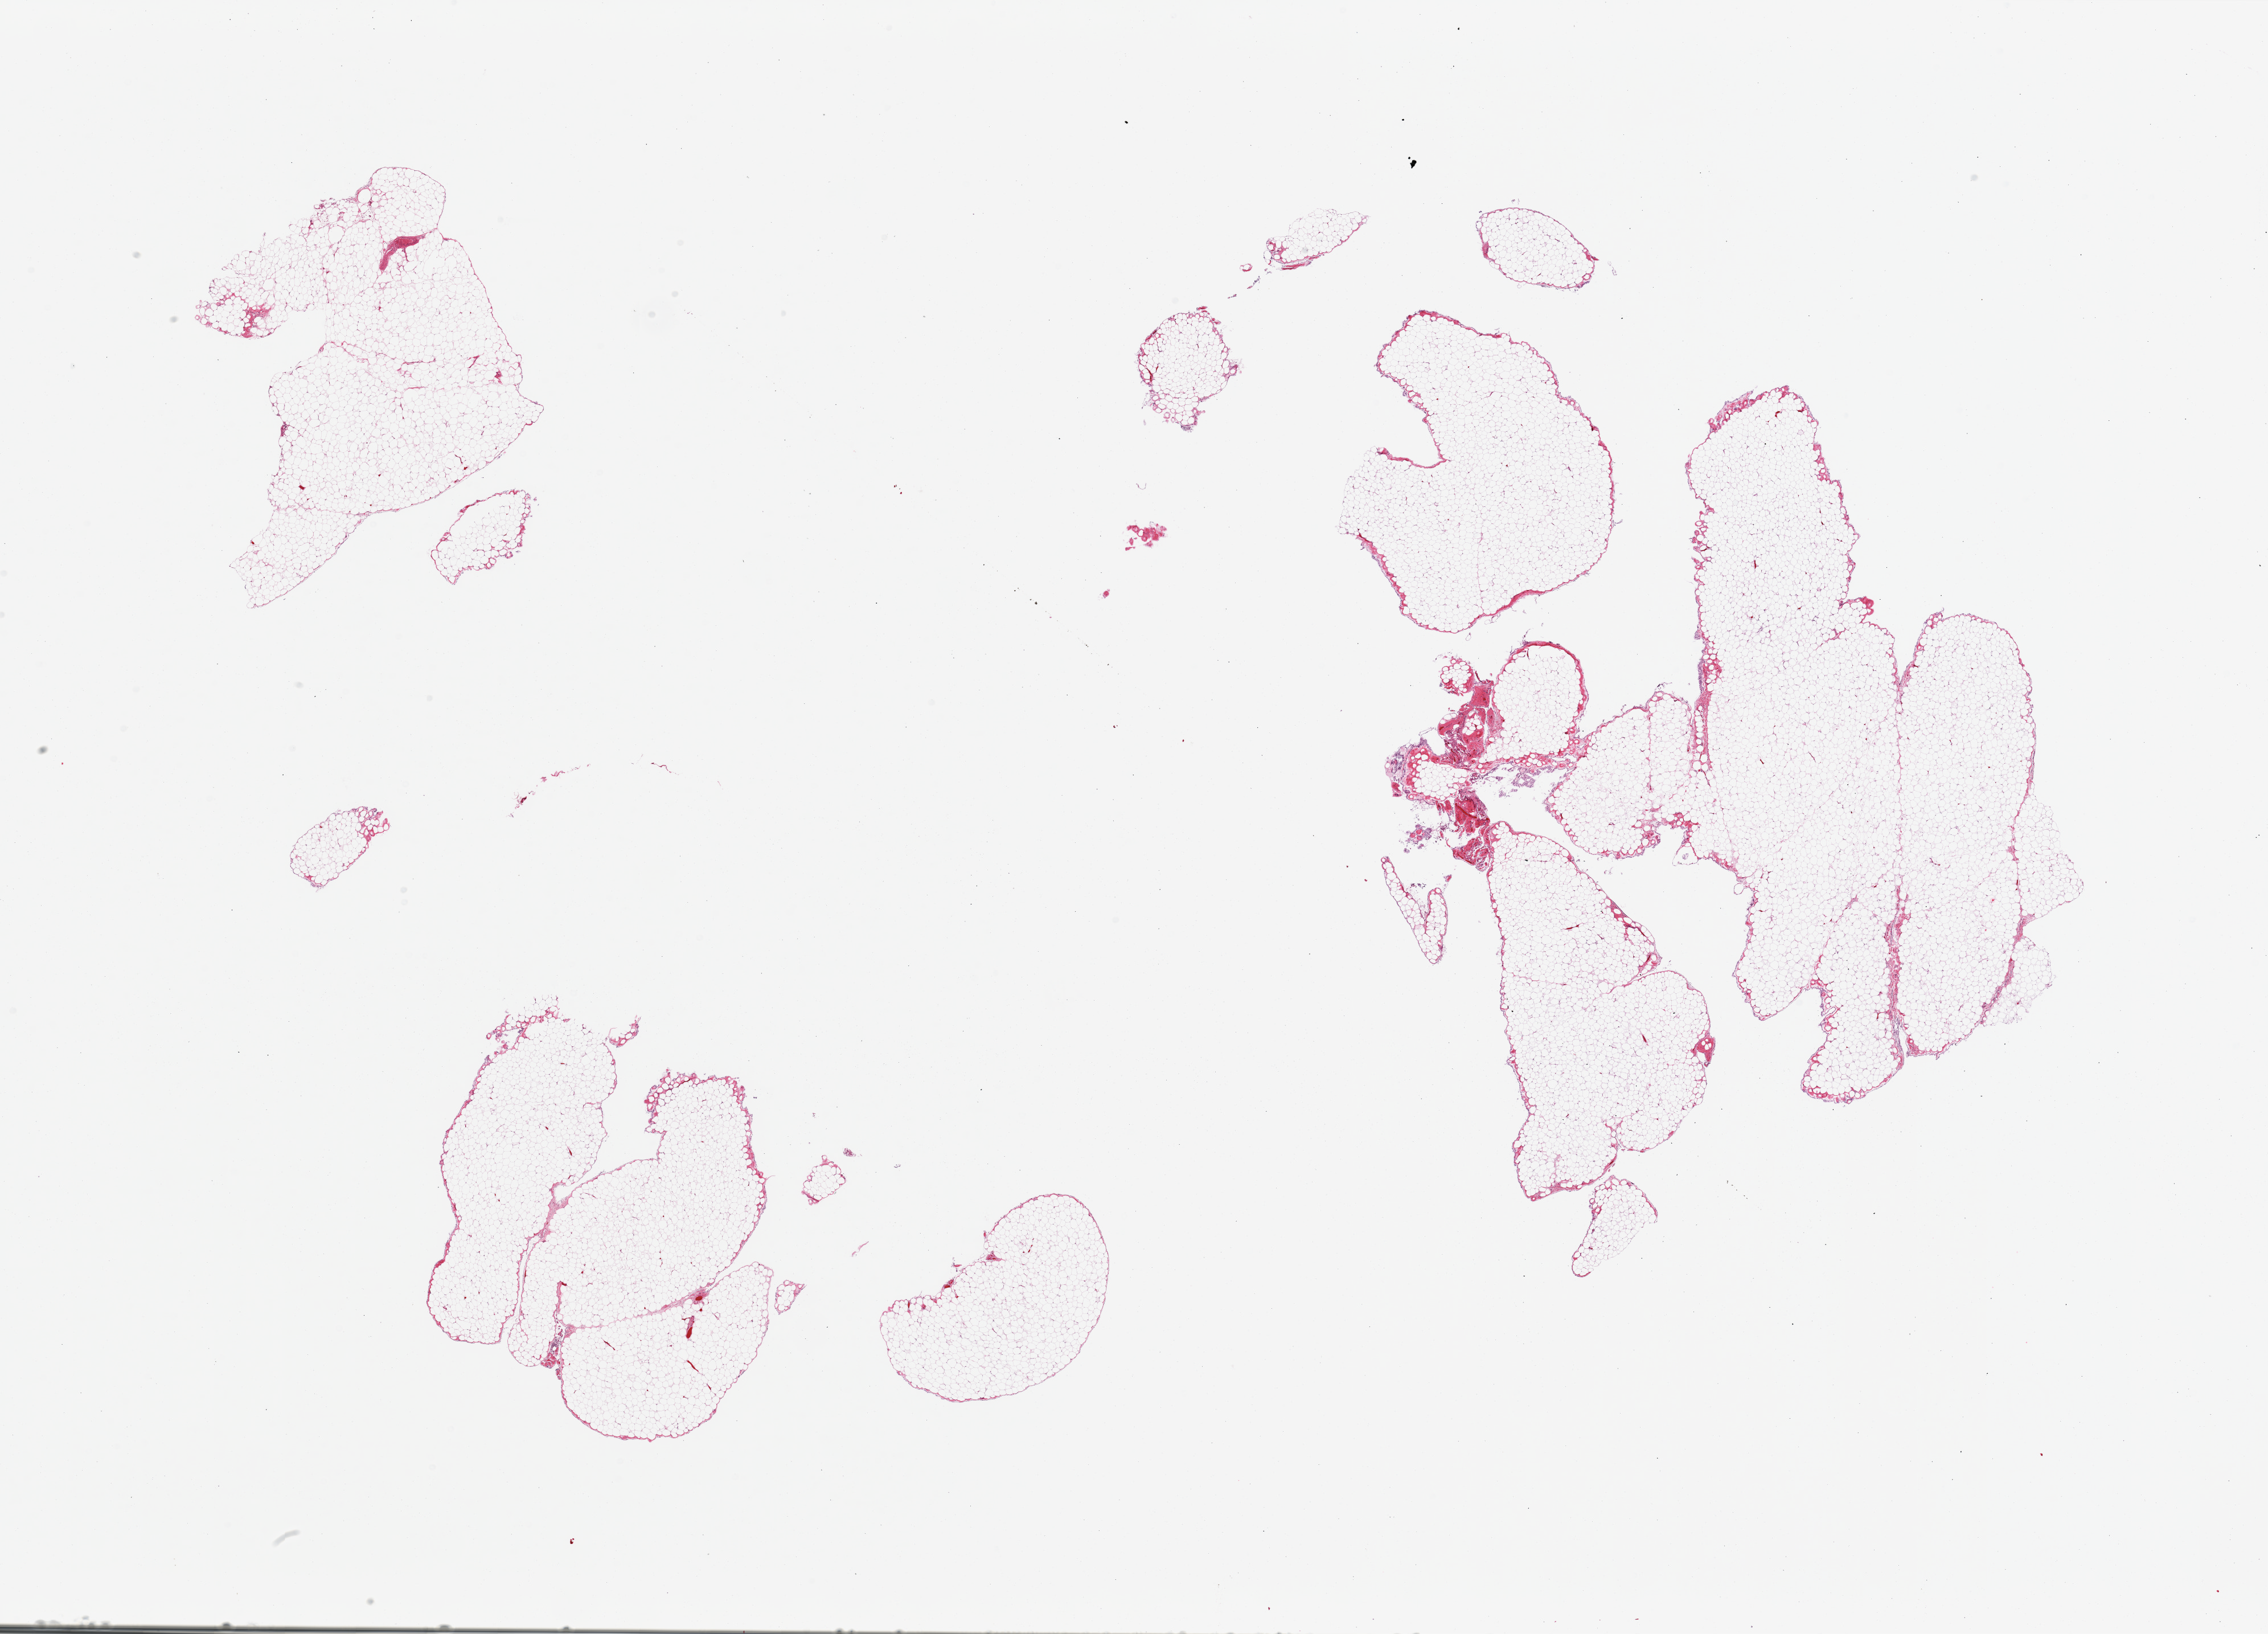
Whole-slide image, H&E stain — shown as a low-resolution overview of the whole scanned area (about 31.5 x 22.7 mm, acquisition: 20x scan). PAXgene-fixed, paraffin-embedded tissue. Target tissue: omentum. Tissue donor sample.
Reviewer comment on this tissue sample: 2 pieces (fragmented); lobulated mature adipose tissue with mesothelial outlines.